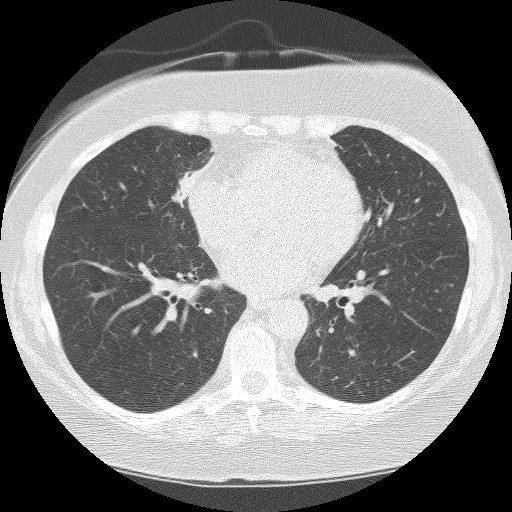
Low-dose screening chest CT, one axial slice. Reconstruction kernel BONE. Lung window (W 1500 / L -600 HU). 2.5 mm slice thickness. 512 × 512 image matrix, field of view 299 × 299 mm.
Structures marked on this image (outlined manually by an expert reader):
- lesion 1 (tumor, hilum of right lung): bounding box <172,156,214,207> (left, top, right, bottom; pixels)